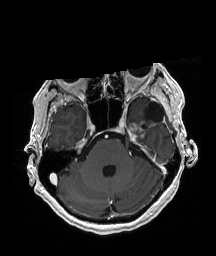
Brain MRI from a brain-tumour surgery series, one axial slice. Slice 137 of 192 in the series (ordered by position). T1-weighted post-contrast. 1 mm slice thickness. 216 × 256 image matrix. From the clinical record (not read from this slice): histopathology: Glioblastoma; WHO grade: 4; IDH mutation: no.
Annotated regions visible in this slice (manually delineated by an expert):
- previous resection cavity: bounding box [x1, y1, x2, y2] px = [147, 102, 163, 122]